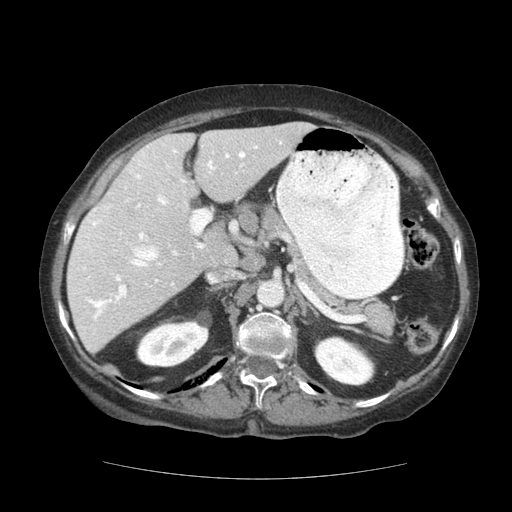
Contrast-enhanced abdominal CT (liver protocol), one axial slice. Slice 73 of 111 in the series (ordered by position). Reconstruction kernel STANDARD. Soft-tissue window (W 400 / L 40 HU). 2.5 mm slice thickness. 512 × 512 image matrix, field of view 360 × 360 mm. Case-level facts recorded for this patient, not image findings: diagnosis: hepatocellular carcinoma (patient treated with transarterial chemoembolisation; whether this scan precedes or follows treatment is not stated here); TNM stage (as recorded): Stage-I; Child-Pugh class: A; tumour differentiation: moderately-poorly differentiated; tumour nodularity: uninodular.
Annotated regions visible in this slice (semi-automatically segmented with operator editing):
- liver parenchyma outside the tumour (the mass and vessels are separate outlines, so this box may not span the whole liver): bounding box (x1, y1, x2, y2) in pixels: (66, 122, 312, 352)
- liver vessels: (83, 141, 282, 320)